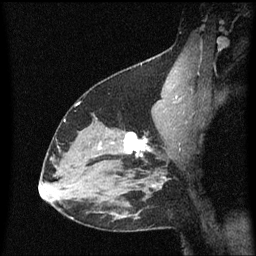
Breast MRI (dynamic contrast-enhanced), one sagittal slice. Position 41 of 60 along the scan axis. Dynamic contrast-enhanced series, image 2 of 3 at this slice position (ordered by acquisition). 1.5 T. TE 4.2 ms, TR 8.4 ms. 256 × 256 image matrix, field of view 200 × 200 mm. Patient: female, 38 years. From the clinical record (not read from this slice): setting: breast cancer imaged before/during neoadjuvant chemotherapy; receptor status: HR-positive, HER2-negative.
Structures marked on this image (semi-automatic segmentation, software-assisted and operator-edited):
- analysis volume of interest (the breast-tissue region the enhancement analysis was run in; not a lesion): bounding box (x1, y1, x2, y2) in pixels: (122, 130, 154, 163)
- tumour enhancement mask (voxels above the 70 % enhancement threshold inside the analysis volume of interest): (125, 132, 152, 157)